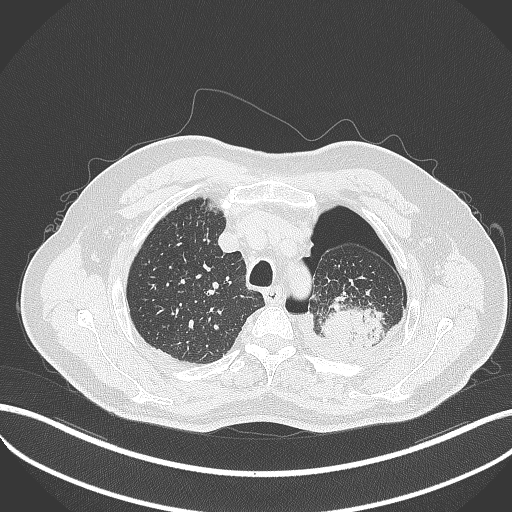
Chest CT, one axial slice; position 409 of 464 along the scan axis; lung window (W 1500 / L -600 HU); 512 × 512 image matrix, field of view 400 × 400 mm. Patient: male, 76 years. From the clinical record (not read from this slice): clinical TNM (as recorded): T3 N0 M1b.
Structures marked on this image (rectangle marked by the reading radiologist):
- lung tumour (recorded histology: adenocarcinoma): box from (x=323, y=298) to (x=391, y=349) px